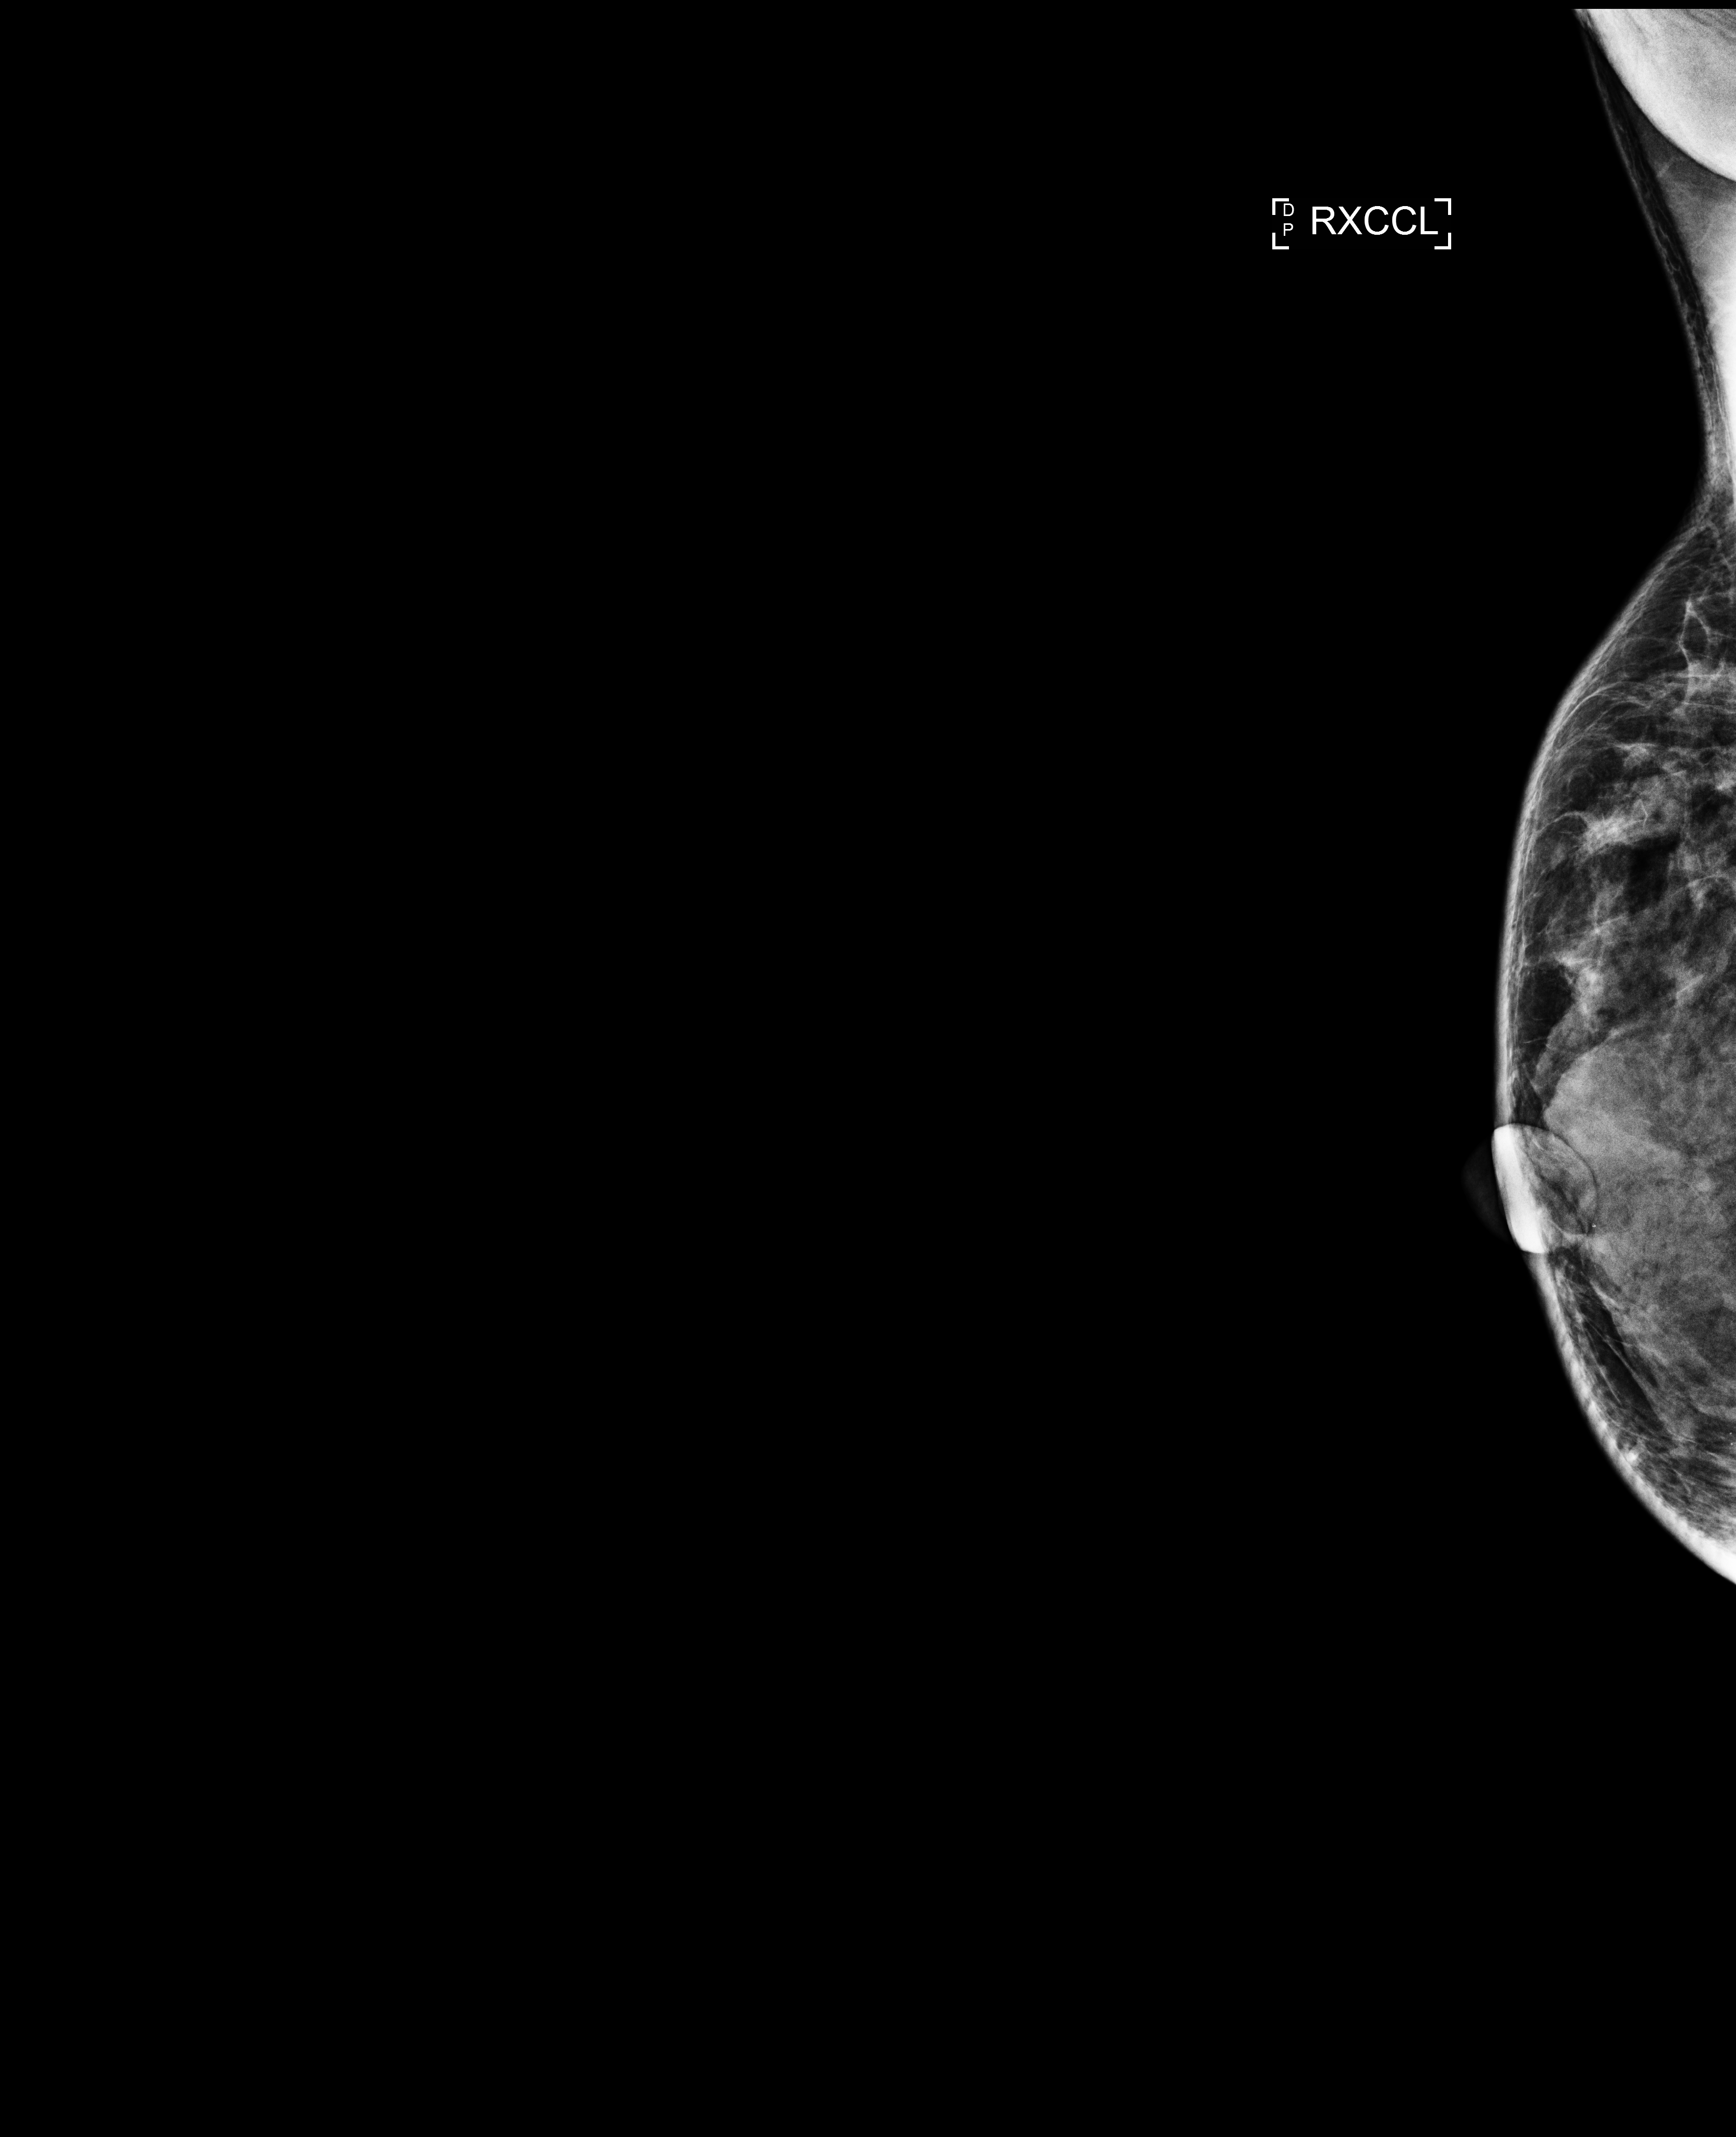
Annual screening mammography examination. Patient aged 60 years (female).
Image type: full-field digital mammogram. Breast: right. Projection: laterally exaggerated craniocaudal (XCCL) view.